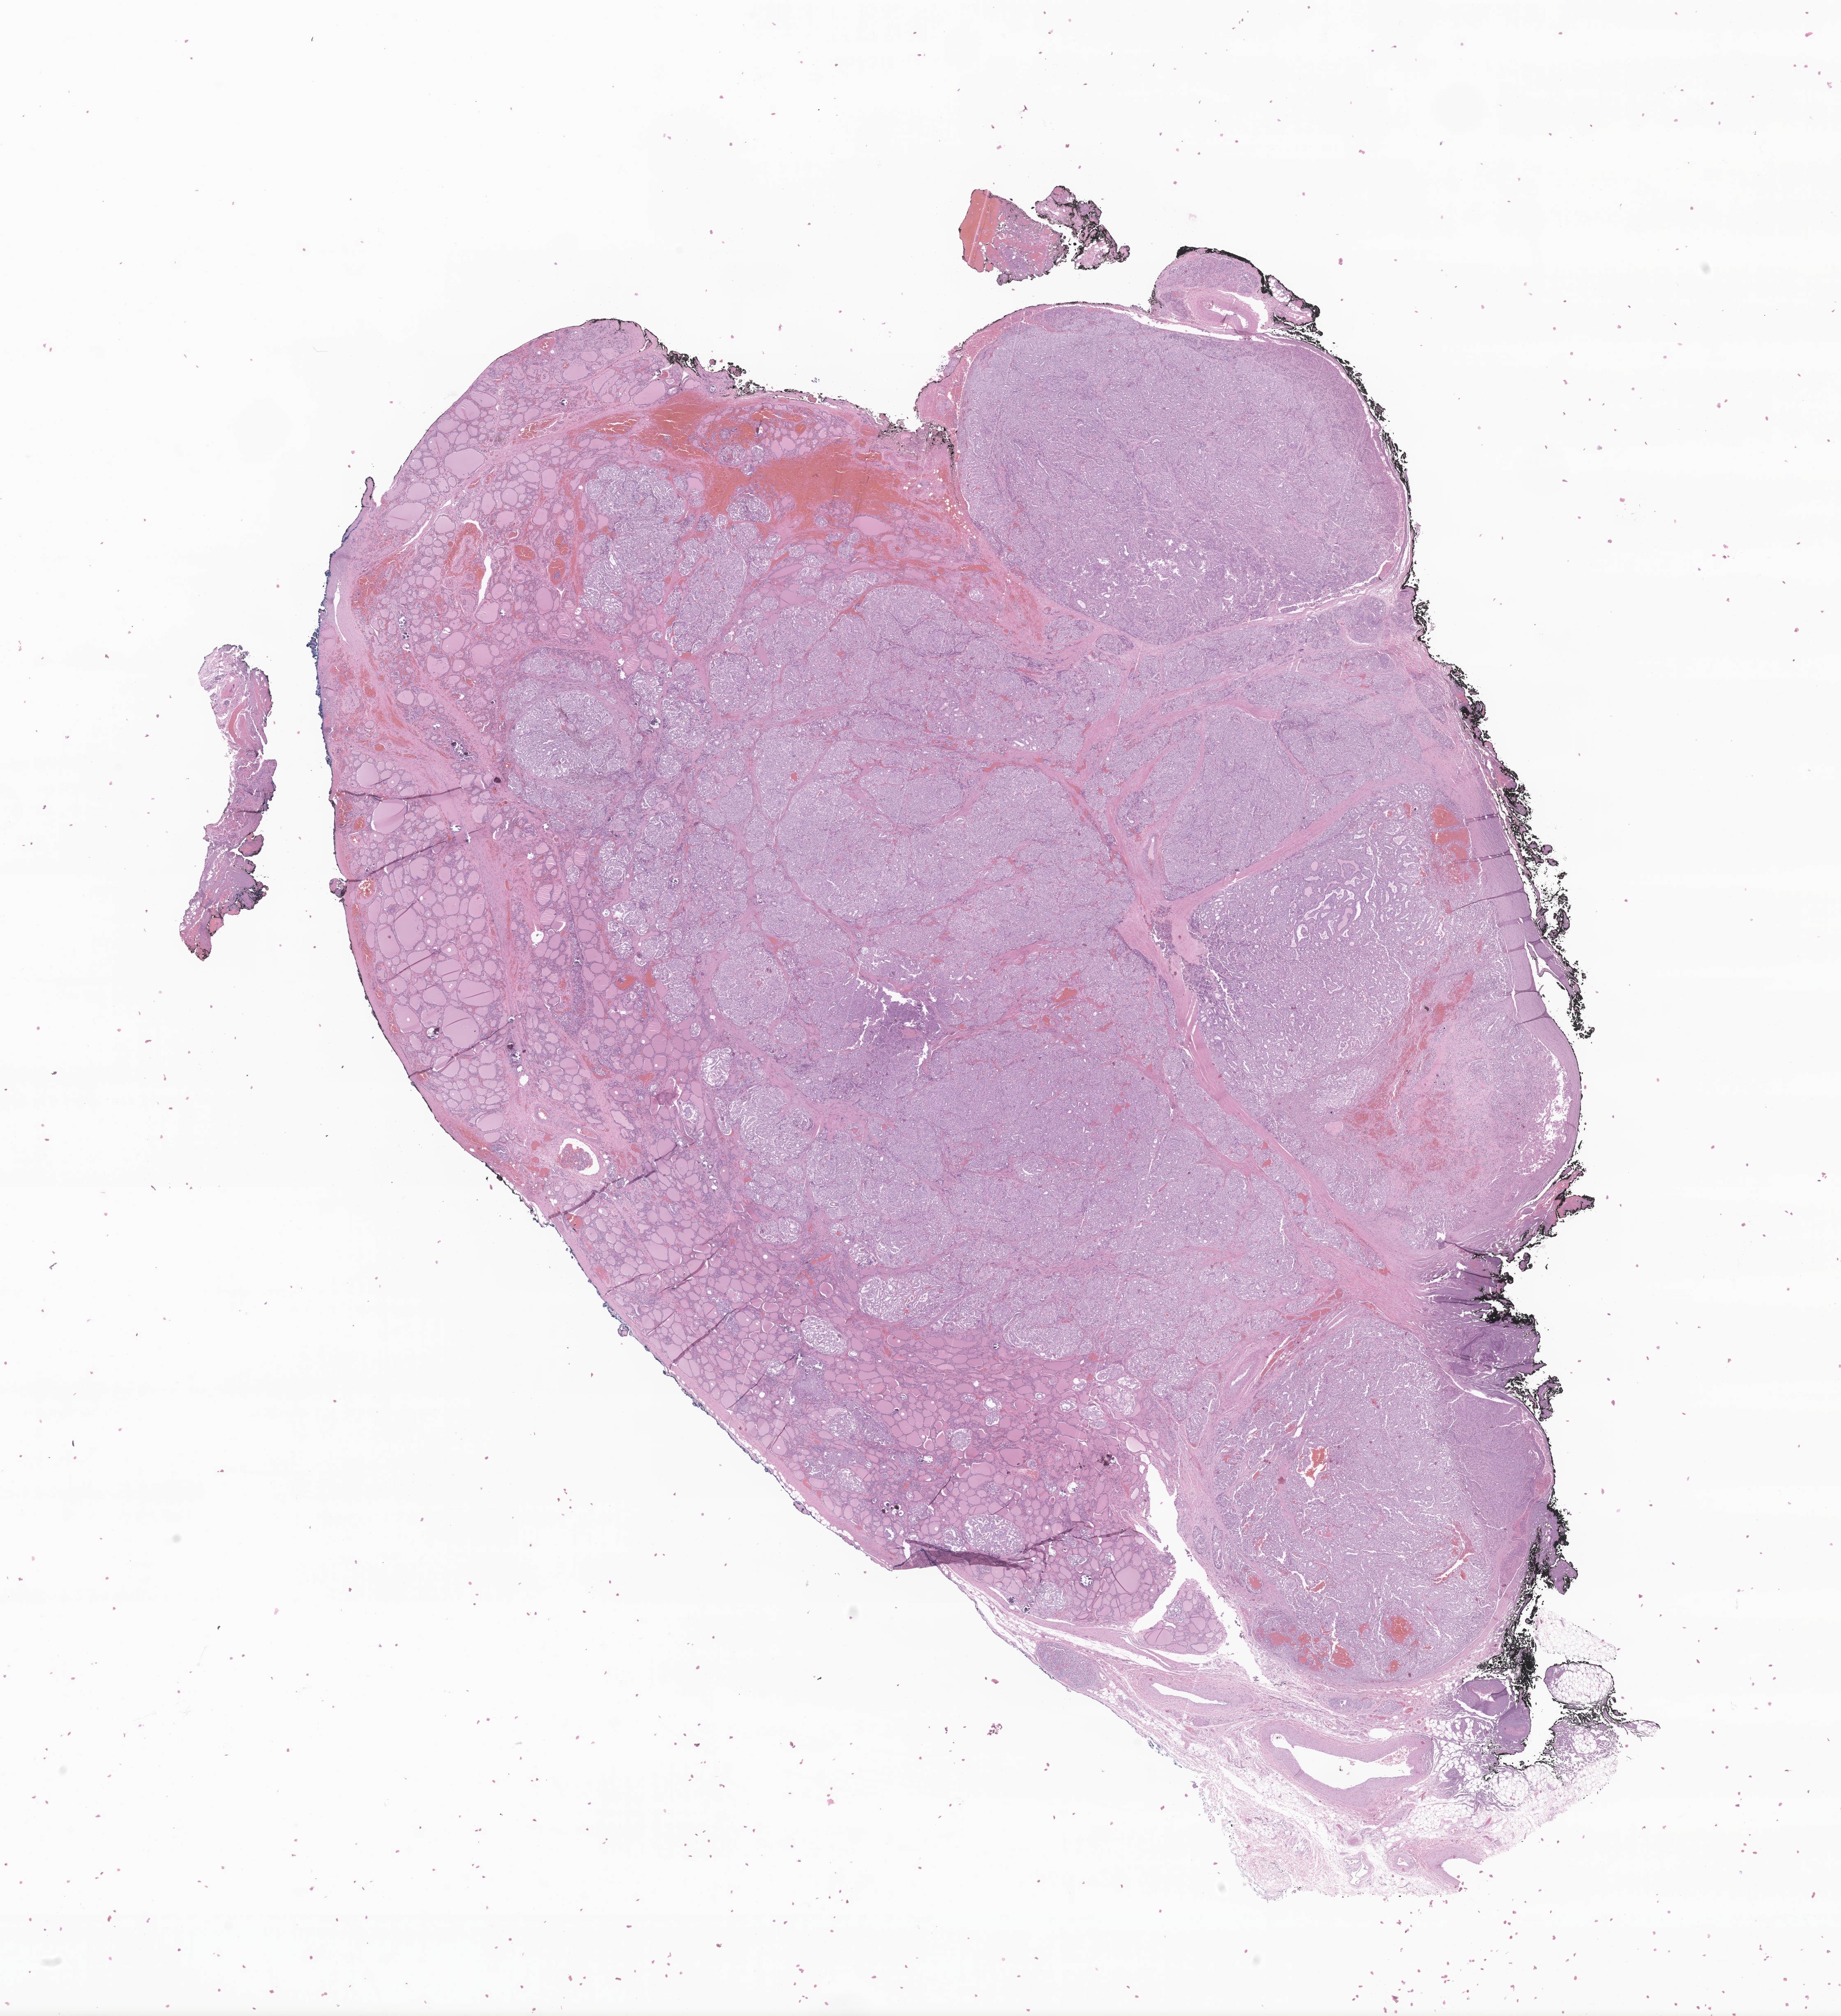
Hematoxylin and eosin (H&E) whole-slide image of tumor tissue from the thyroid — whole scanned area (about 18.9 x 20.7 mm) shown as a low-resolution overview. FFPE section. Patient male; age 142 months.
* diagnosis (ICD-O-3 morphology term): Papillary carcinoma, NOS